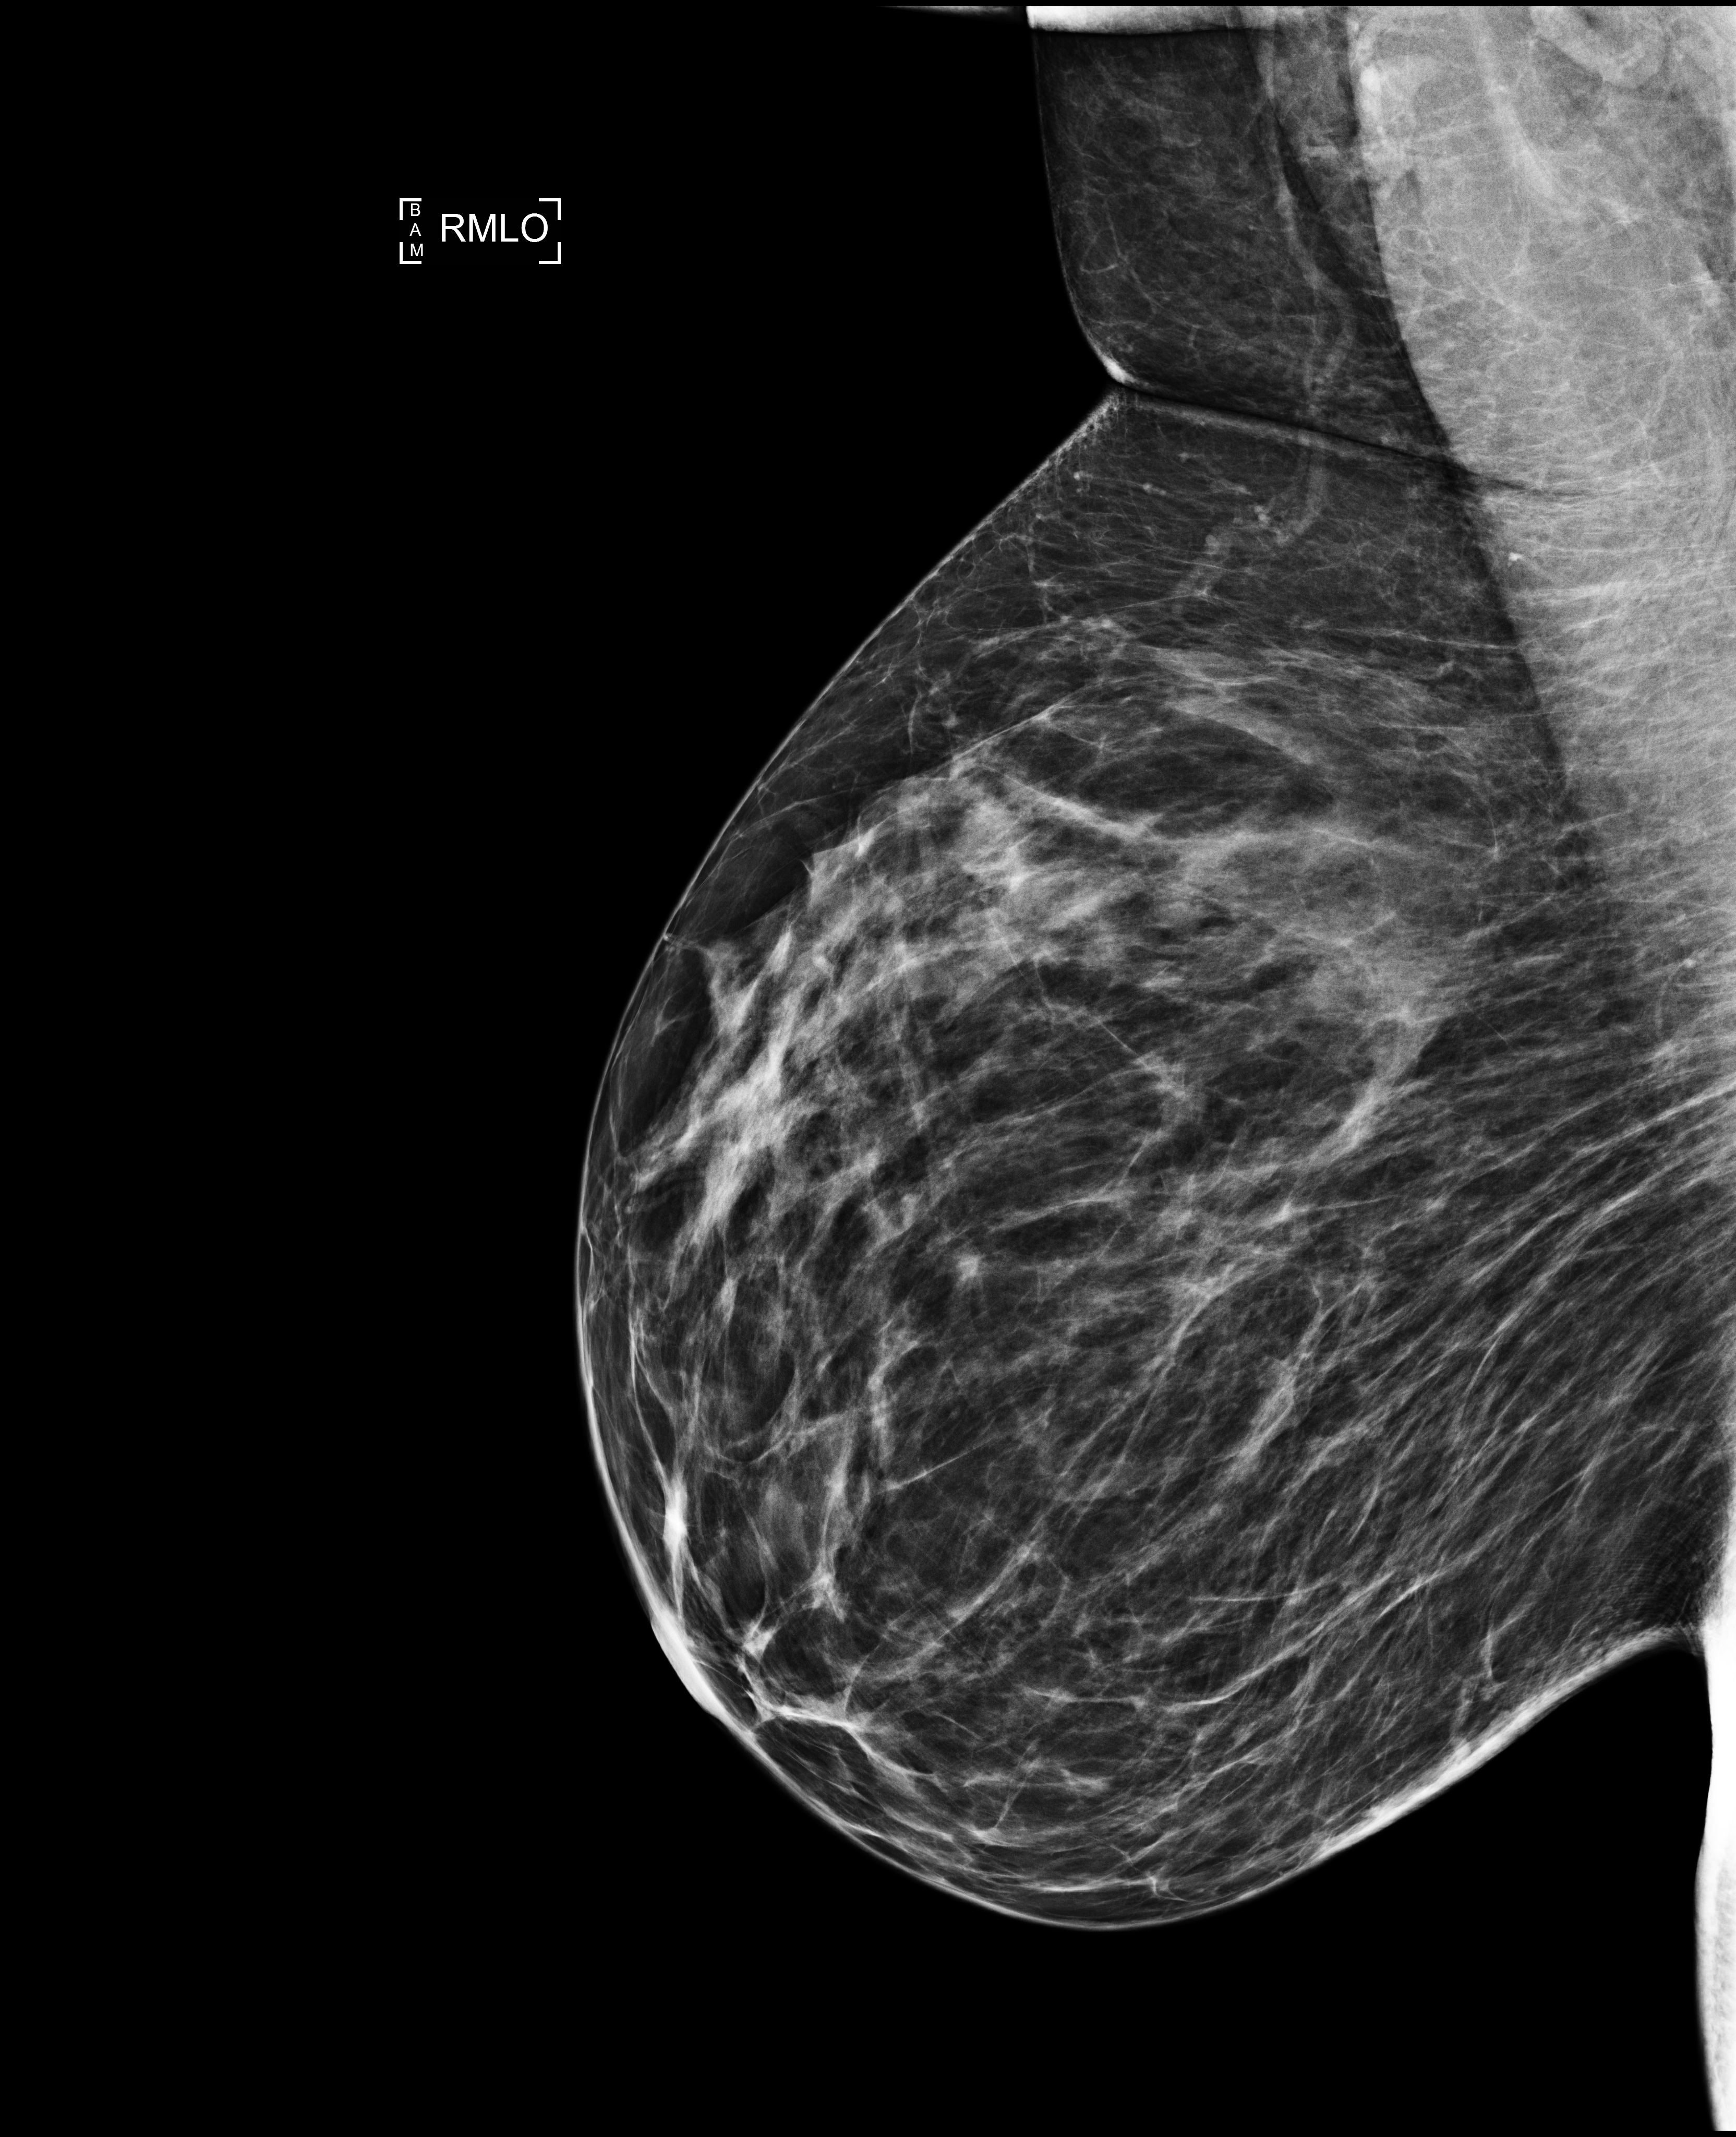
Digital mammogram (FFDM); right breast; mediolateral oblique (MLO) view; screening examination; compressed breast thickness 76 mm. Female patient, age 42 years.
Final BI-RADS category for the screening round (tomosynthesis exam, both breasts): category 1.